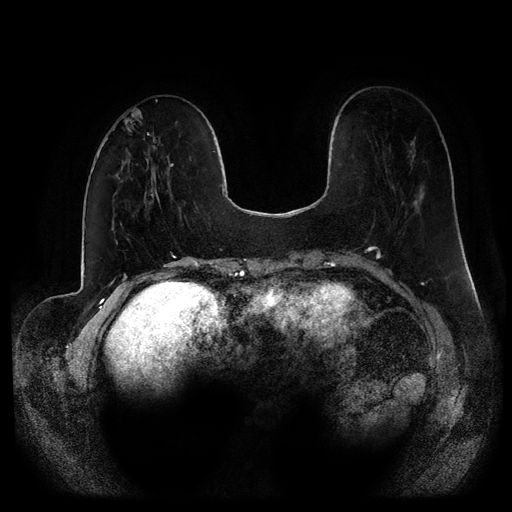
Breast MRI (dynamic contrast-enhanced, multi-phase), one axial slice; position 30 of 116 along the scan axis; dynamic contrast-enhanced series, time point 2 of 5 at this slice position (early post-contrast); 1.5 T; TE 2.6 ms, TR 5.2 ms; 2 mm slice thickness; 512 × 512 image matrix, field of view 380 × 380 mm. Female patient, age 53 years.
Structures marked on this image (semi-automatic segmentation, software-assisted and operator-edited):
- breast lesion (labelled 'tumour' in the annotation; benign lesions carry a separate 'benign' label): bounding box [x1, y1, x2, y2] px = [125, 108, 143, 136]